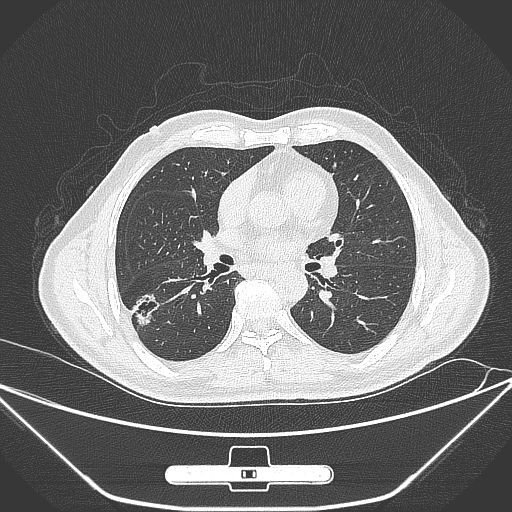
Chest CT, one axial slice. Position 149 of 310 along the scan axis. 120 kVp. Lung window (W 1500 / L -600 HU). 1 mm slice thickness. 512 × 512 image matrix, field of view 398 × 398 mm. Patient: male, 71 years. From the clinical record (not read from this slice): clinical TNM (as recorded): T1c N0 M0; histopathological grade: G2.
Outlined on this slice (rectangle marked by the reading radiologist):
- lung tumour (recorded histology: adenocarcinoma): bounding box (x1, y1, x2, y2) in pixels: (132, 291, 174, 333)